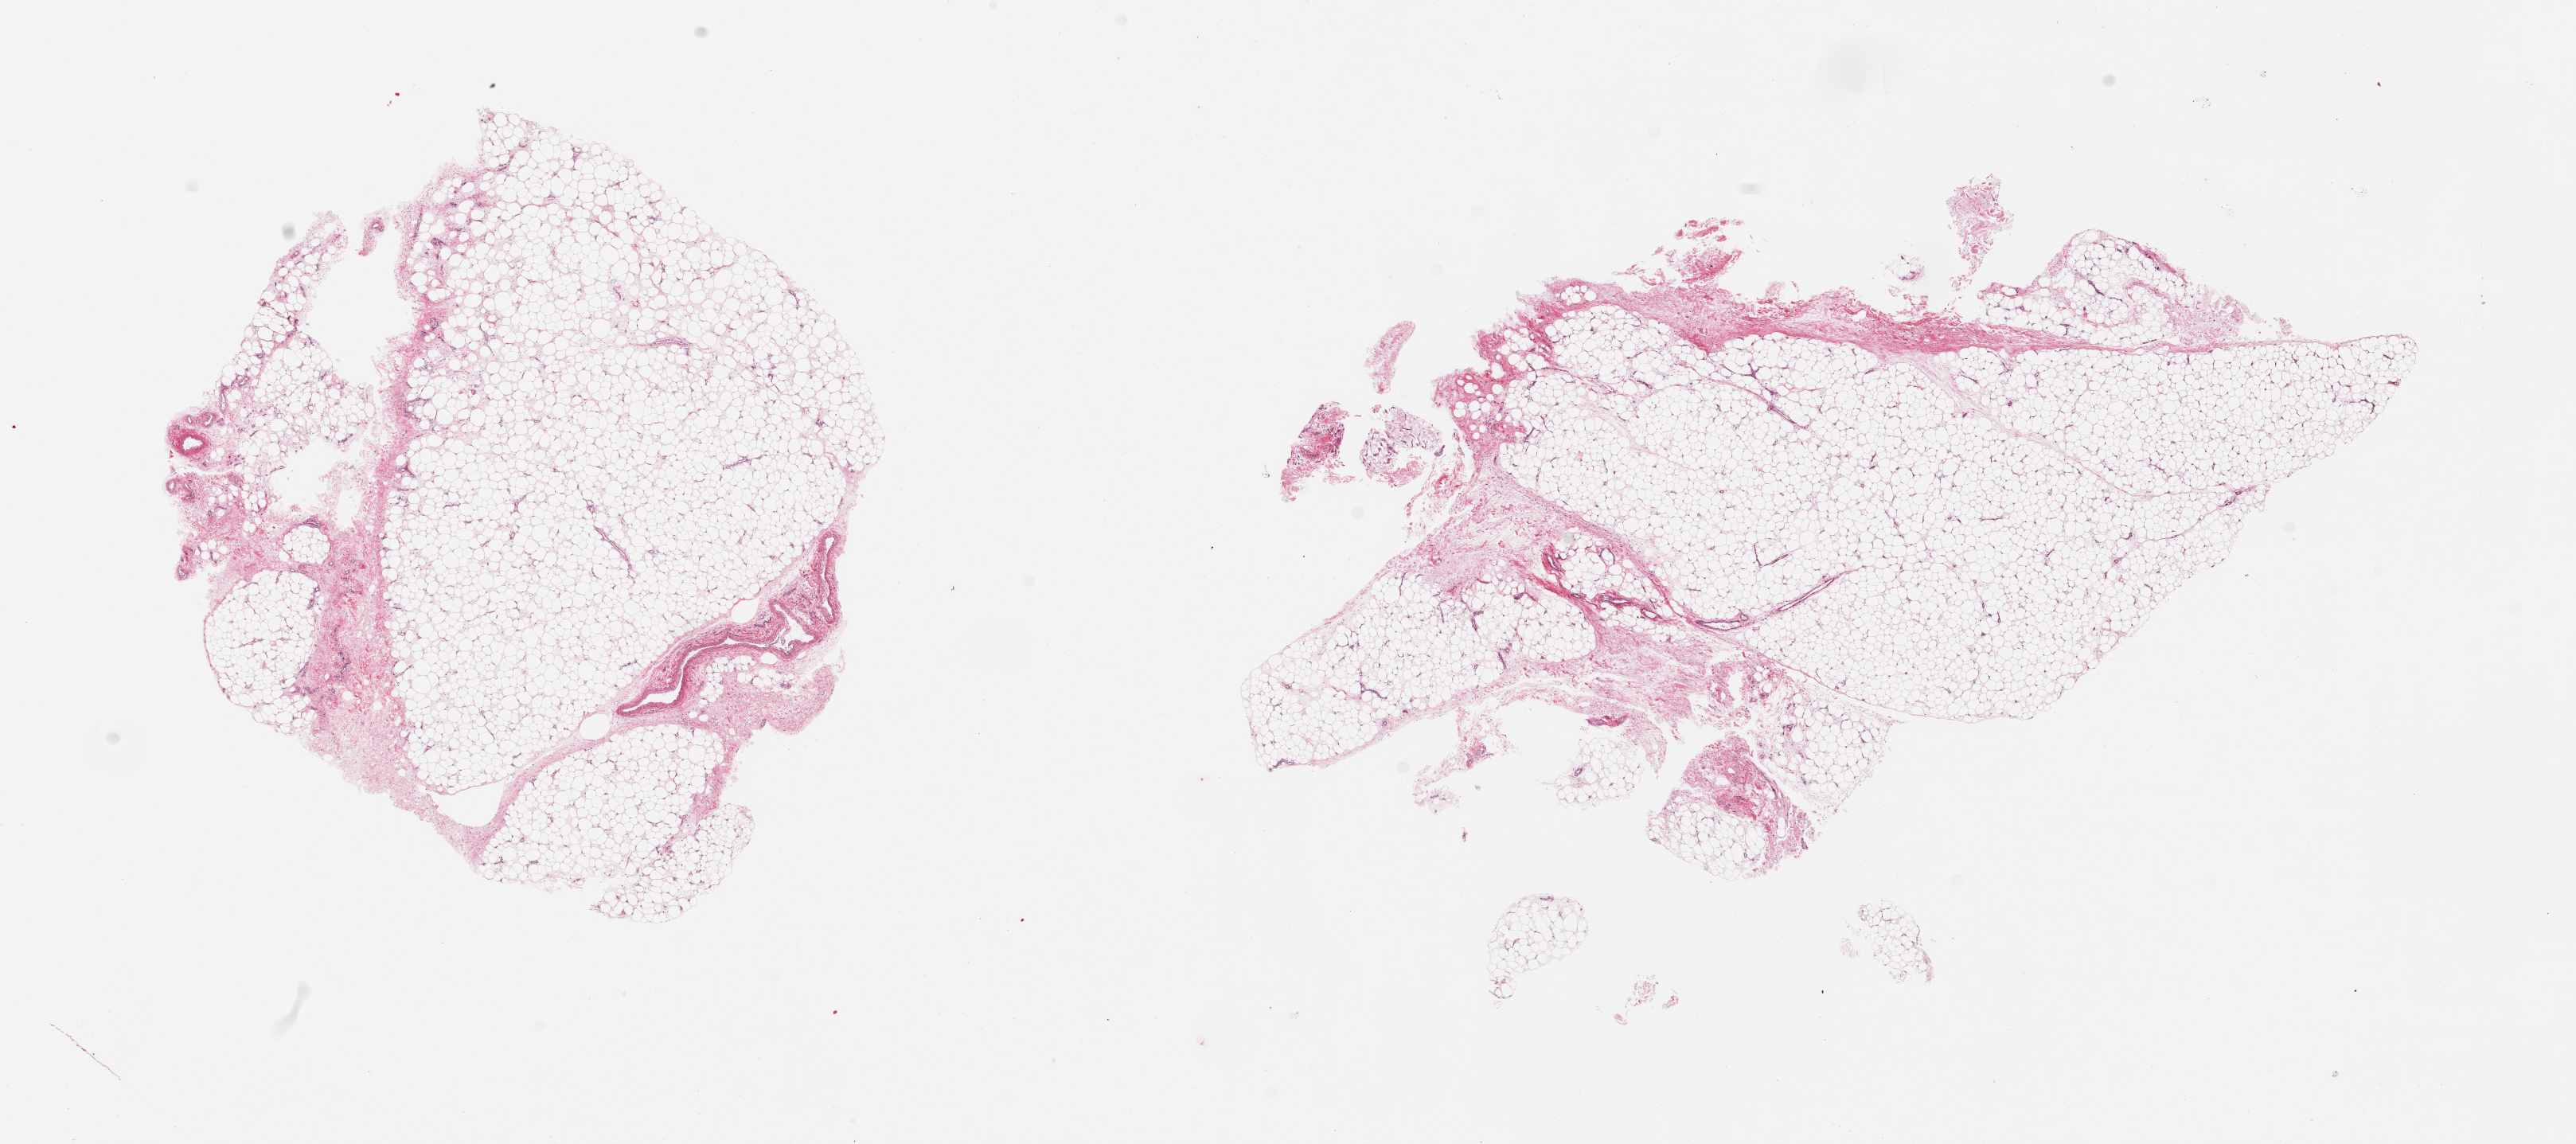
Digitized haematoxylin and eosin-stained section — whole scanned area (about 25.6 x 11.4 mm, acquisition: 20x scan) shown as a low-resolution overview; PAXgene-fixed paraffin-embedded (PFPE) section; target tissue: adipose tissue; tissue donor sample. Female donor.
• reviewer comment on this tissue sample: 2 pieces; fat with ~10% fibrous/vessels